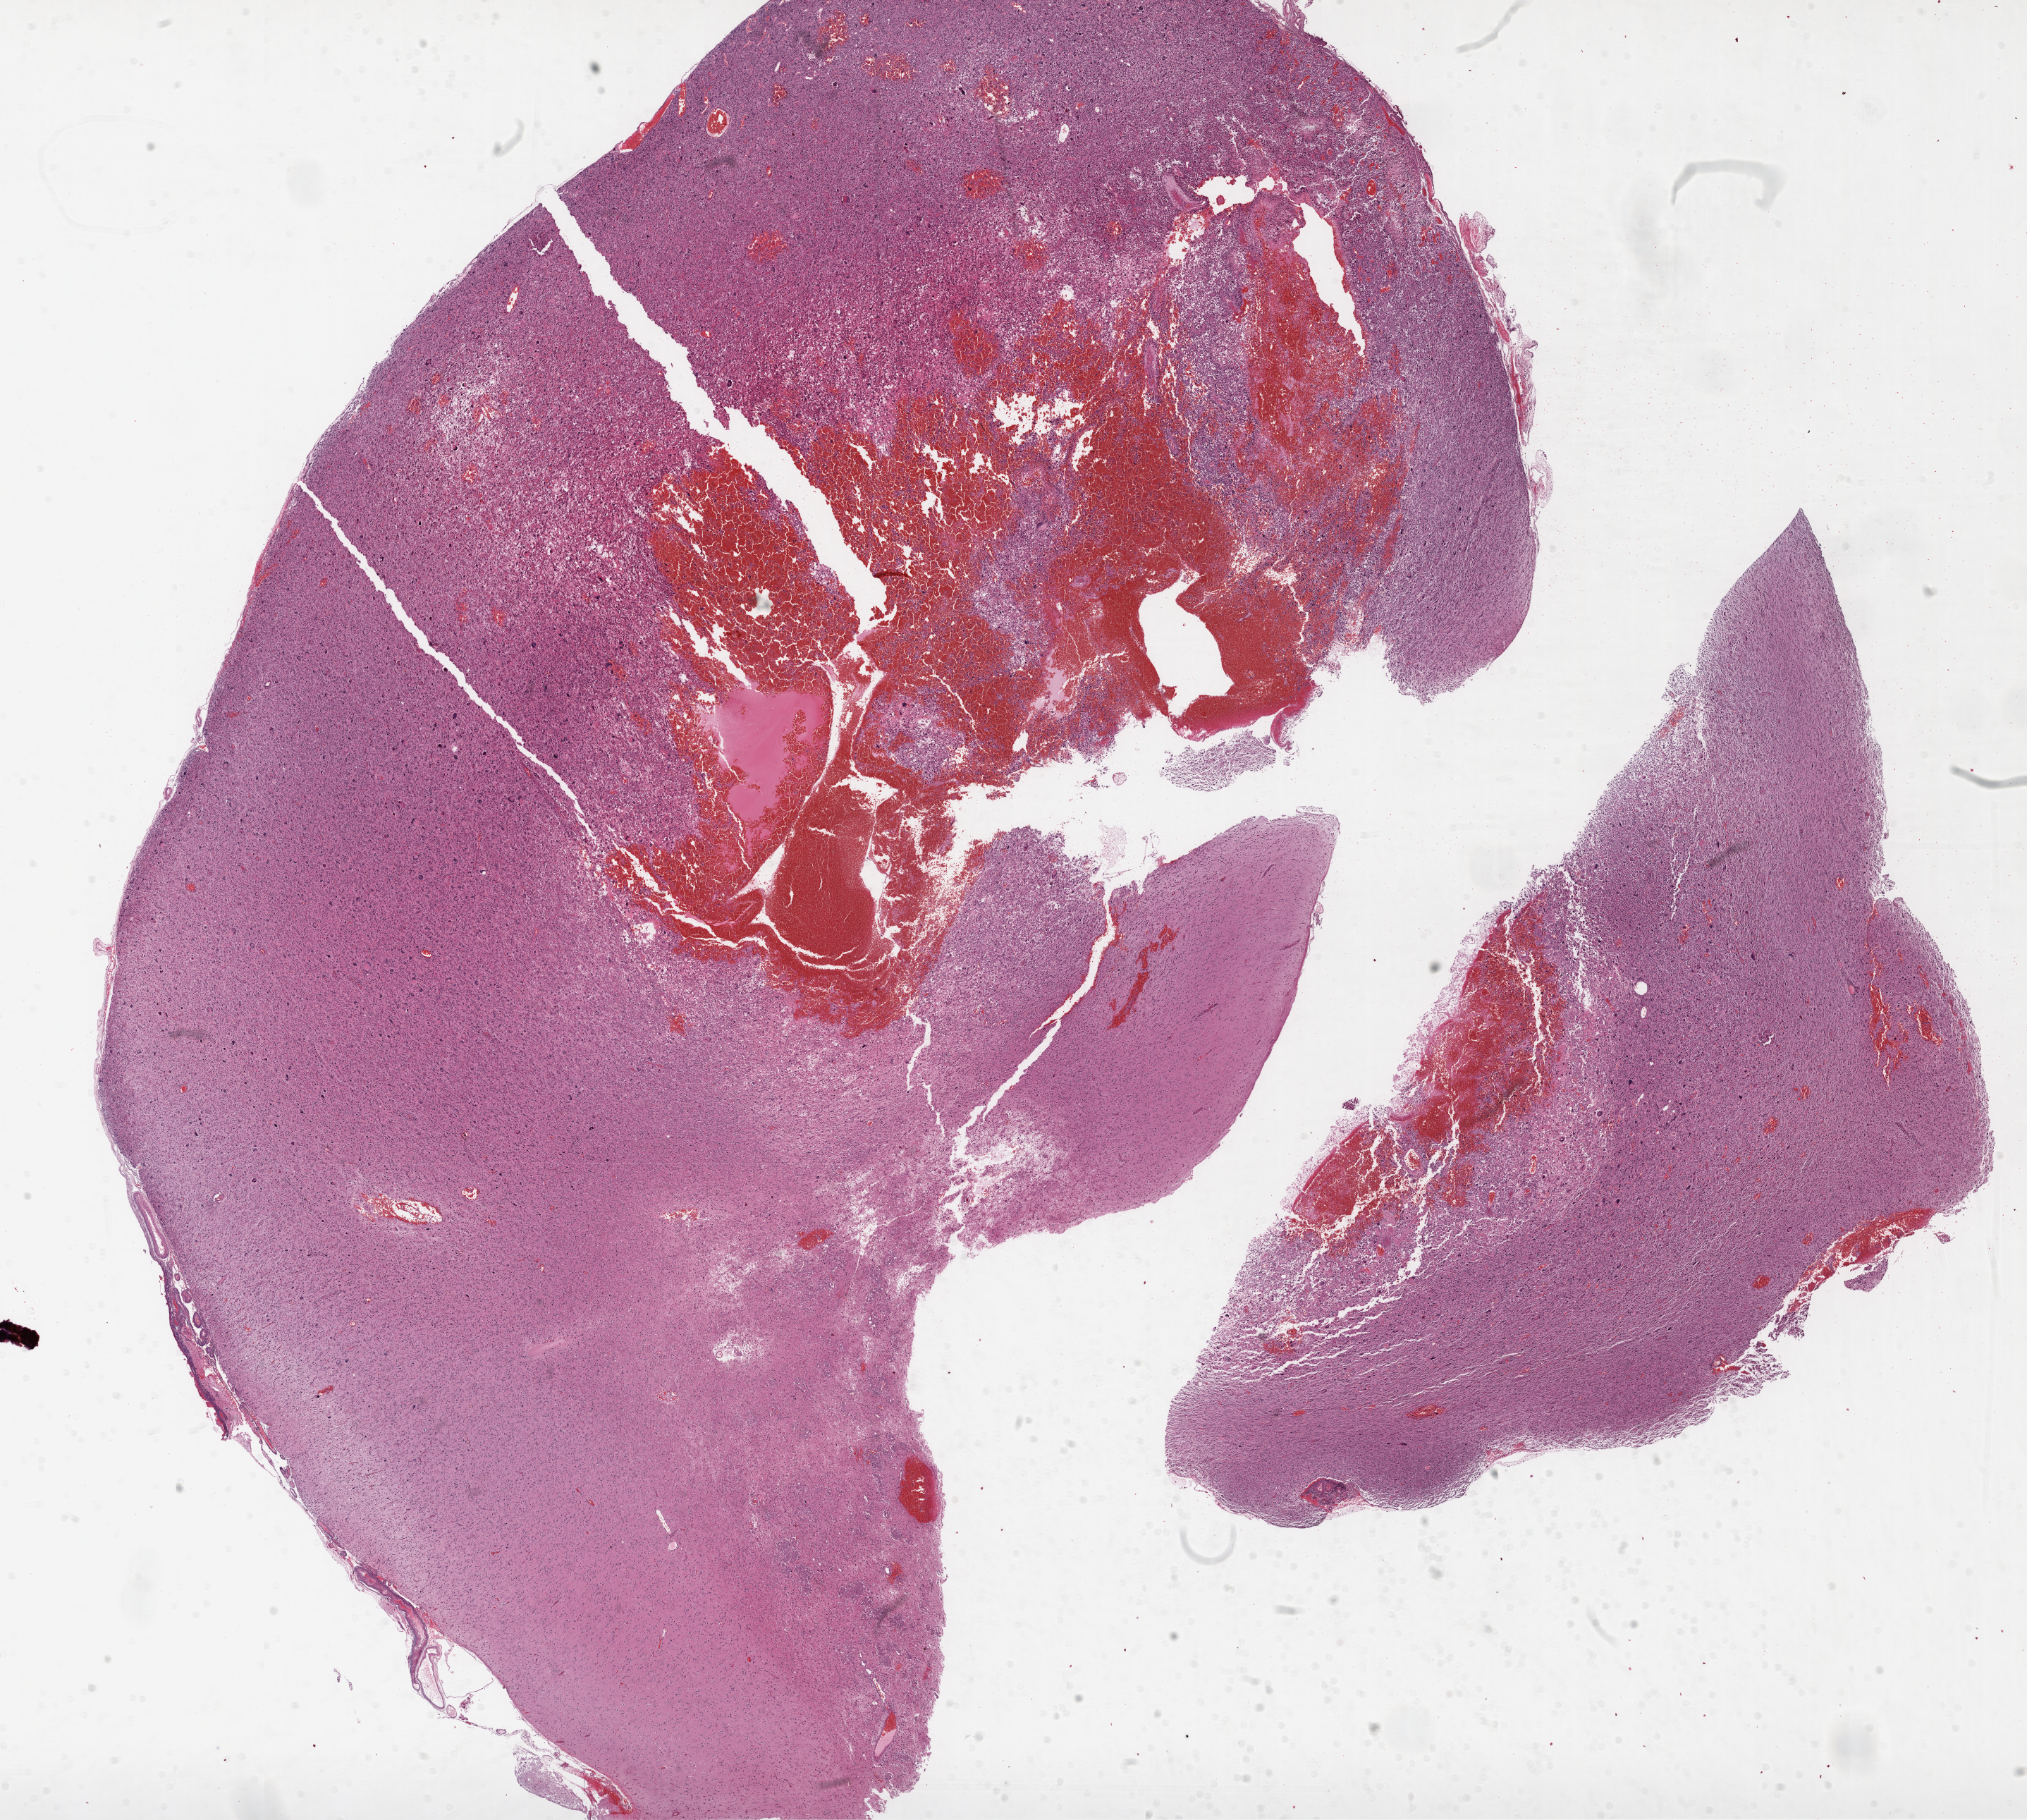
Whole-slide histology image, Hematoxylin and eosin (H&E) stained — whole scanned area (about 23.1 x 20.7 mm, acquisition: 20x scan) shown as a low-resolution overview; formalin-fixed paraffin-embedded (FFPE) diagnostic section; brain, primary tumour sample. Patient: male, age at initial diagnosis 69 years.
Pathologic diagnosis: Glioblastoma.